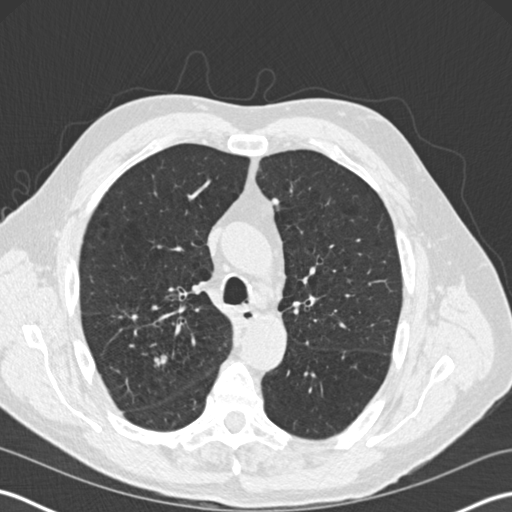
Low-dose screening chest CT, axial slice, third screening round (two years after baseline), lung window (W 1500 / L -600 HU), 2 mm slice thickness, standard (soft-tissue) reconstruction kernel (B30f), 120 kVp, slice 69 of 199 in the series. Male participant, aged 65 years at enrolment. Former smoker at enrolment.
• Lesion marked by an expert reader, bounding box <140,348,182,386> (left, top, right, bottom; pixels).
• The screening reader recorded 6 non-calcified nodules or masses ≥4 mm on this exam (right upper lobe, left upper lobe, left upper lobe, left upper lobe, right upper lobe); which of them this box marks is not recorded.
• Participant outcome: lung cancer diagnosed 78 days after this screen — adenocarcinoma, NOS, right upper lobe, moderately differentiated (G2), stage IA (AJCC 6th edition), 16 mm at pathology.